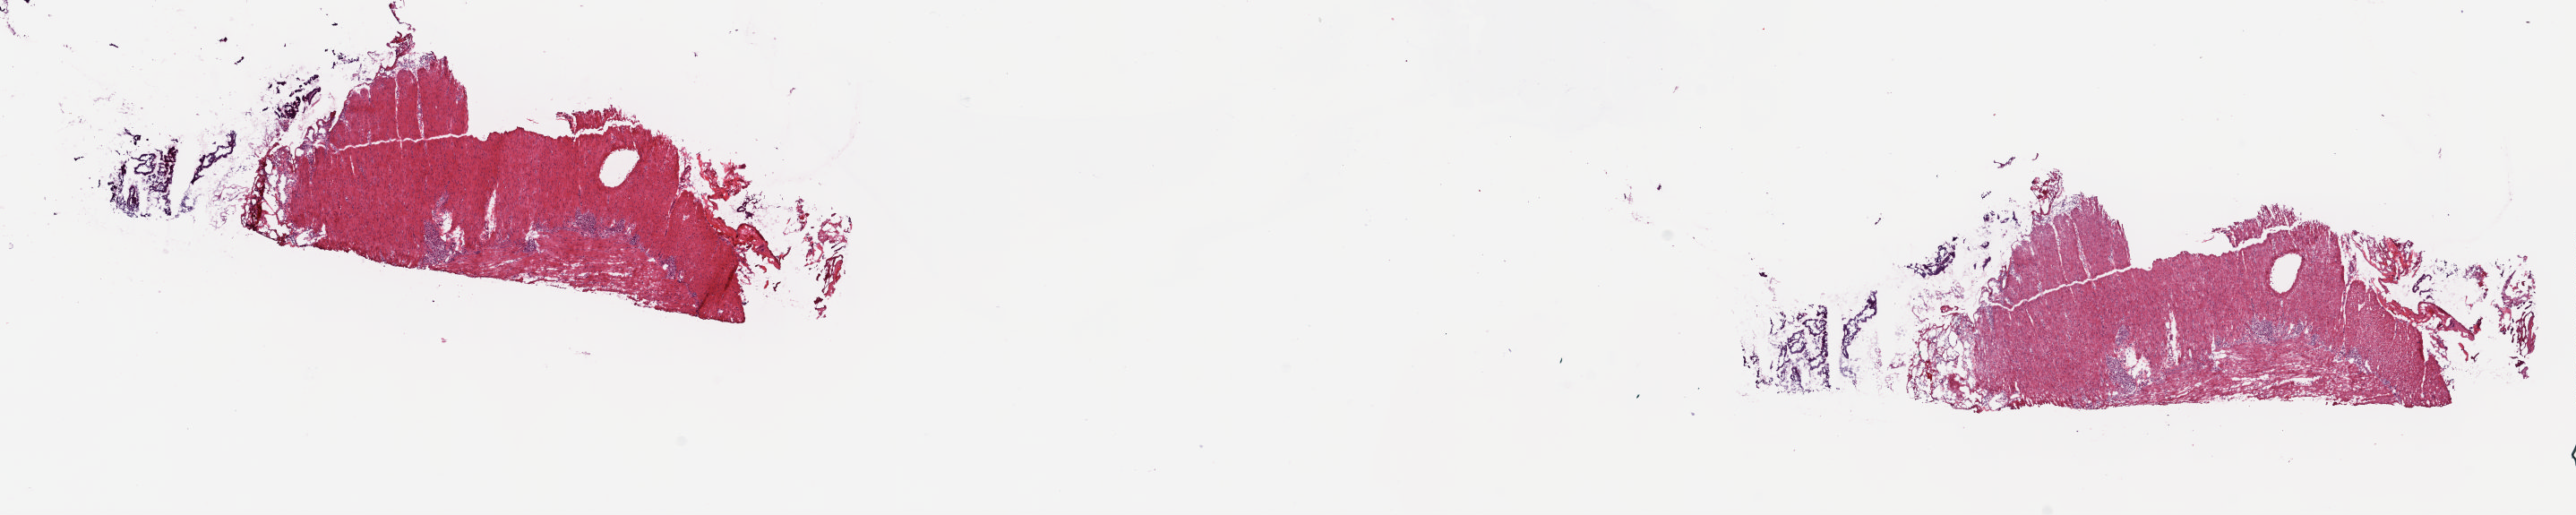
Whole-slide histology image, Hematoxylin and eosin (H&E) stained, low-resolution overview of the scanned area, about 22.8 x 4.6 mm (from a 20x scan), frozen section from the top of the tissue portion, solid tissue normal (non-tumour tissue) sample from the pancreas. Female, age 76 years at initial diagnosis. Slide review estimates, as recorded: tumour cells 0%, tumour nuclei 0%, normal cells 100%, stromal cells 0%, necrosis 0%. Inflammatory infiltration, as recorded: lymphocyte infiltration 0%, monocyte infiltration 0%, neutrophil infiltration 0%.
This section: solid tissue normal sample (biorepository sample class). Patient diagnosis: Infiltrating duct carcinoma, NOS (head of pancreas).